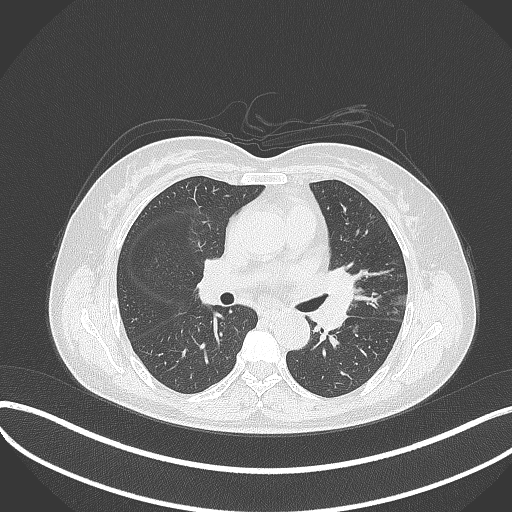
Chest CT, one axial slice. Position 195 of 373 along the scan axis. Reconstruction kernel B70f. 120 kVp. Lung window (W 1500 / L -600 HU). 512 × 512 image matrix, field of view 400 × 400 mm. Patient: female, 54 years. Case-level facts recorded for this patient, not image findings: clinical TNM (as recorded): T2a N1 M0; histopathological grade: G3.
Structures marked on this image (rectangle marked by the reading radiologist):
- lung tumour (recorded histology: small cell carcinoma): bounding box (x1, y1, x2, y2) in pixels: (319, 268, 356, 336)